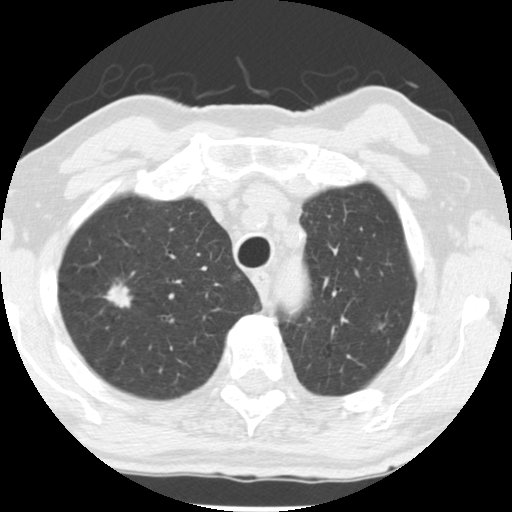
Axial slice from a low-dose chest CT screening exam; first (baseline) screen; lung window (W 1500 / L -600 HU); 120 kVp; slice 205 of 252 in the series; 512 × 512 image matrix, field of view 313 × 313 mm. Male, age 69 years at enrolment.
• Expert-annotated lung lesion, bounding box <90,270,149,328> (left, top, right, bottom; pixels).
• The screening reader recorded 2 non-calcified nodules or masses ≥4 mm on this exam (right upper lobe, left upper lobe); which of them this box marks is not recorded.
• Official screen result: positive, change unspecified: nodule(s) >= 4 mm or enlarging nodule(s), mass(es), or other non-specific abnormalities suspicious for lung cancer.